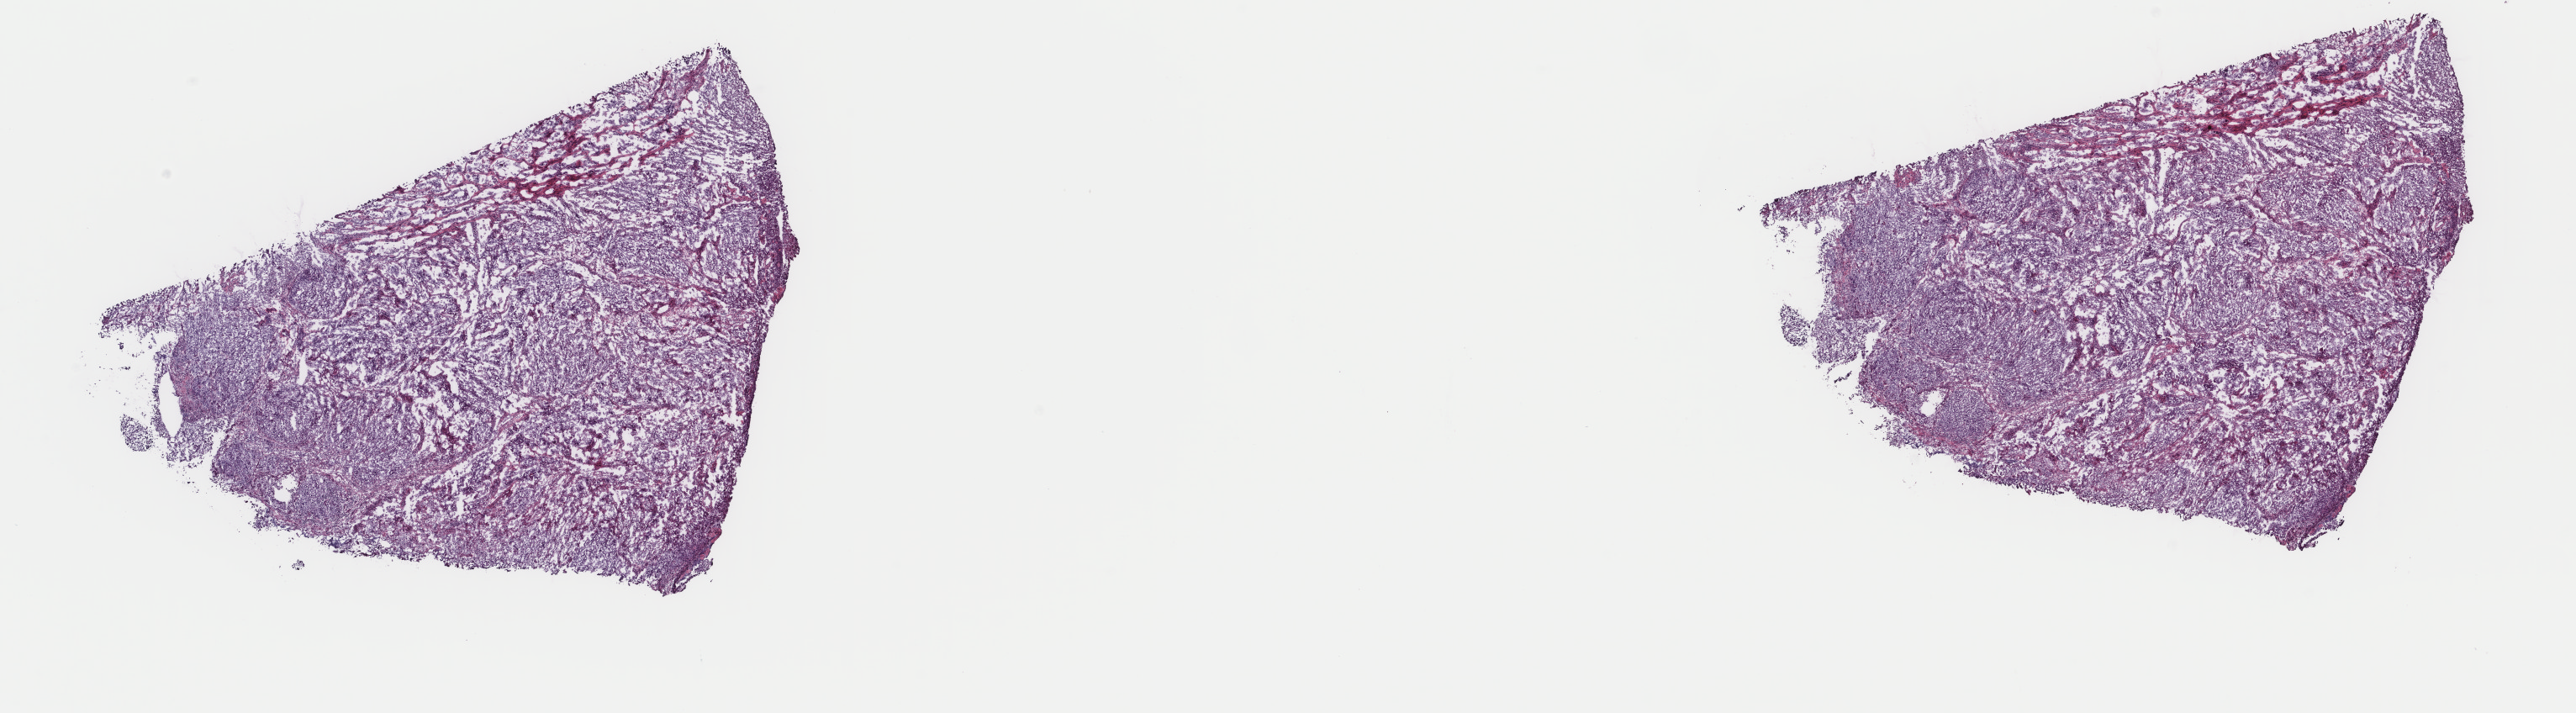
Hematoxylin and eosin (H&E) stained whole-slide image — low-resolution overview of the scanned area, about 24.3 x 6.7 mm (from a 40x scan); frozen section from the top of the tissue portion; sample: primary tumour, bladder. Patient: male, age at initial diagnosis 80 years. Histologic grade: high grade. Composition of this section per pathologist review: tumour cells 60%, tumour nuclei 60%, normal cells 0%, stromal cells 39%, necrosis 1%. Infiltration values recorded for this section: lymphocyte infiltration 9%, monocyte infiltration 6%, neutrophil infiltration 6%.
Lymph nodes positive (case pathology): 0 of 3 examined. AJCC pathologic stage: II. Pathologic diagnosis: Transitional cell carcinoma (posterior wall of bladder).